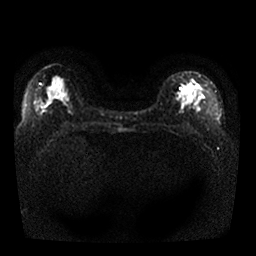
Breast MRI, one axial slice; slice 13 of 25 in the series (ordered by position); diffusion-weighted series; image 2 of 4 stored at this slice position (different b-values; order by instance number); 1.5 T; 4 mm slice thickness; 256 × 256 image matrix, field of view 330 × 330 mm. Female patient.
Structures marked on this image (manually delineated by an expert):
- tumour on diffusion-weighted imaging: bounding box <184,79,205,99> (left, top, right, bottom; pixels)